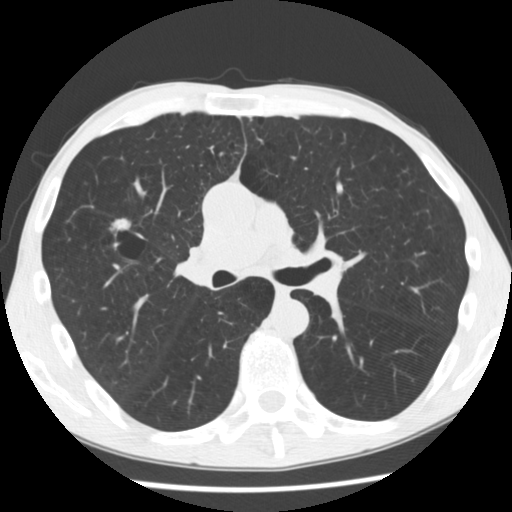
Low-dose screening chest CT, axial slice. Baseline annual screen. Lung window (W 1500 / L -600 HU). 2.5 mm slice thickness. 512 × 512 image matrix, field of view 330 × 330 mm. Male, age 56 years at enrolment. Current smoker at enrolment.
Expert-annotated lung lesion, box from (x=98, y=206) to (x=151, y=252) px. The screening reader recorded 2 non-calcified nodules or masses ≥4 mm on this exam (right upper lobe, right upper lobe); which of them this box marks is not recorded. Later outcome: lung cancer diagnosed 476 days after this screen — squamous cell carcinoma, NOS, right upper lobe, right middle lobe, well differentiated (G1), stage IA (AJCC 6th edition), 27 mm at pathology.